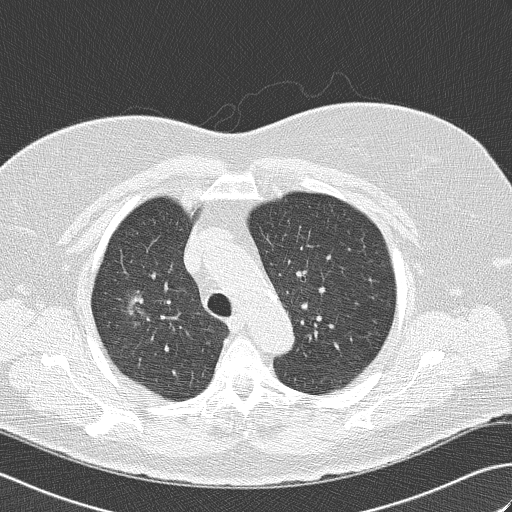
Low-dose screening chest CT, axial slice; second screening round (one year after baseline); lung window (W 1500 / L -600 HU); lung (sharp) reconstruction kernel (B50f); slice 116 of 148 in the series. Female participant, aged 74 years at enrolment.
Lesion marked by an expert reader, box from (x=104, y=280) to (x=165, y=333) px. The screening reader recorded 4 non-calcified nodules or masses ≥4 mm on this exam (right upper lobe, right middle lobe, right middle lobe, left lower lobe); which of them this box marks is not recorded. Lung cancer was diagnosed 453 days after this screen (after the third annual screen): bronchiolo-alveolar carcinoma, non-mucinous, right upper lobe, well differentiated (G1), stage IA (AJCC 6th edition), 14 mm at pathology.